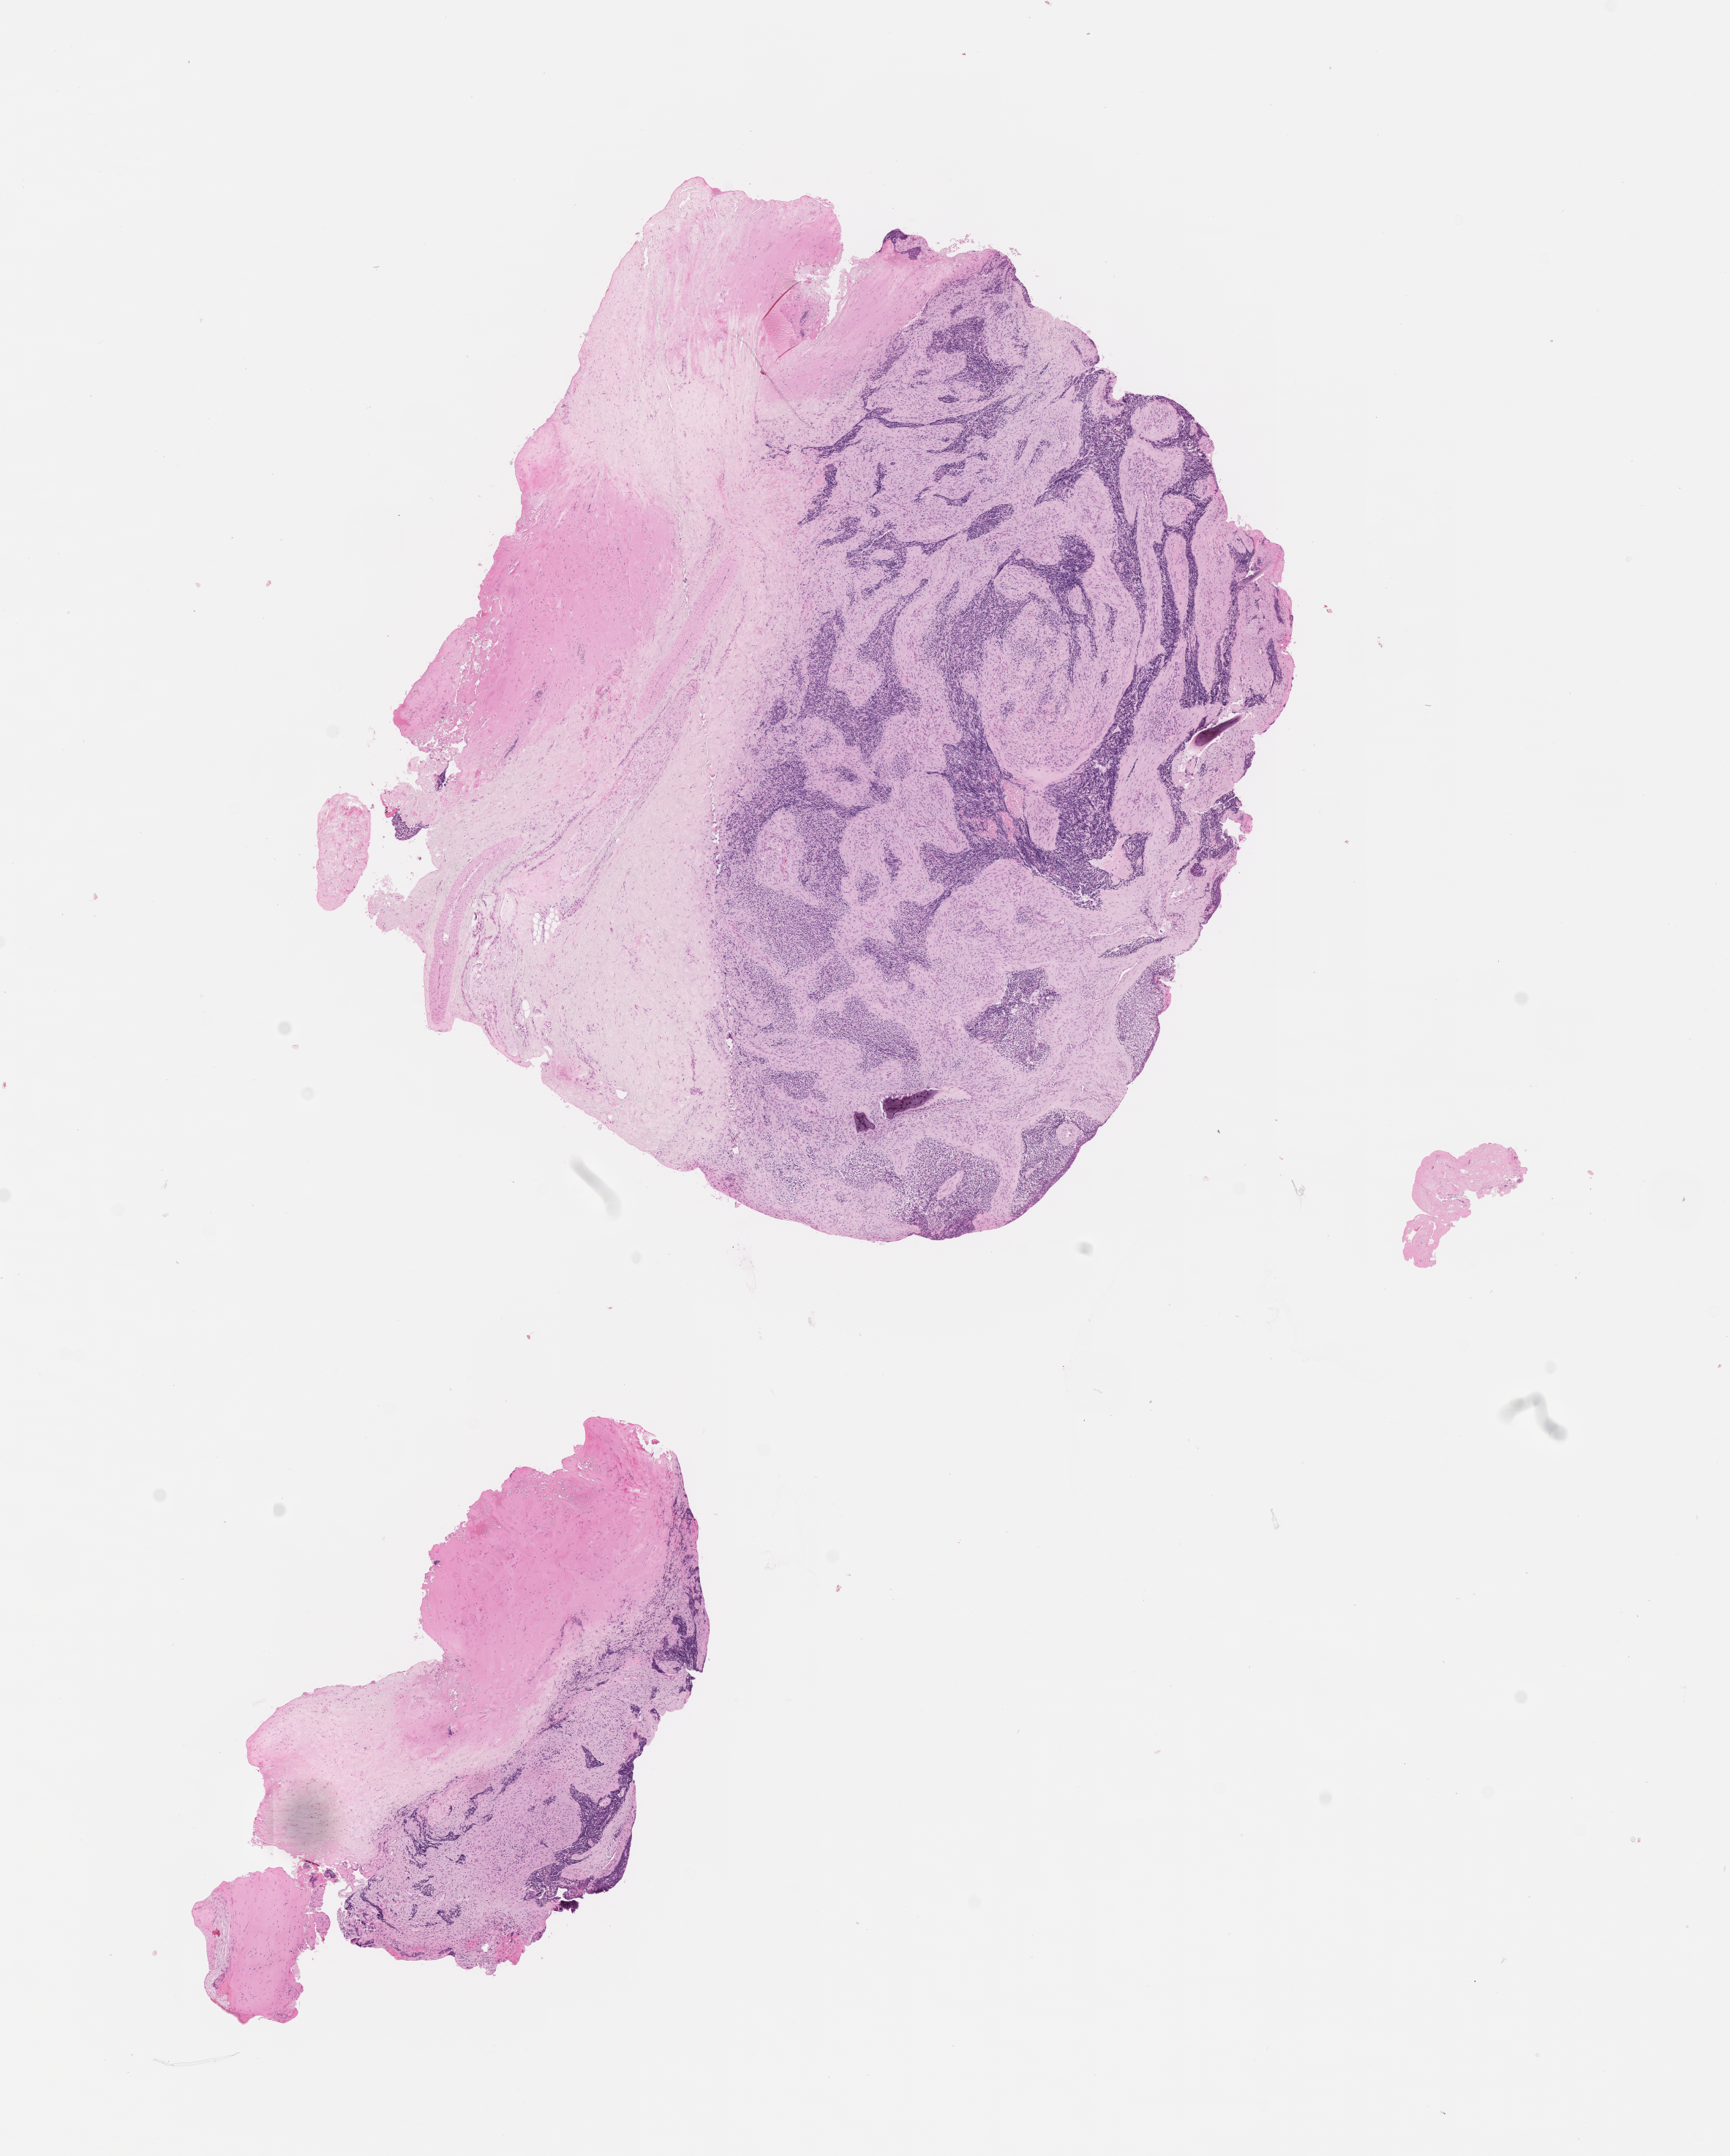
Digitized H&E-stained section of tumor tissue — low-resolution overview of the scanned area, about 9.6 x 11.9 mm. FFPE section. Site: soft tissue, orbit. Patient: male, age 2.3 years at diagnosis.
* metastatic status at presentation (as recorded): non-metastatic
* diagnosis: rhabdomyosarcoma; histological classification: embryonal rhabdomyosarcoma
* stage (as recorded): 3
* primary site (case record): infratemporal Fossa